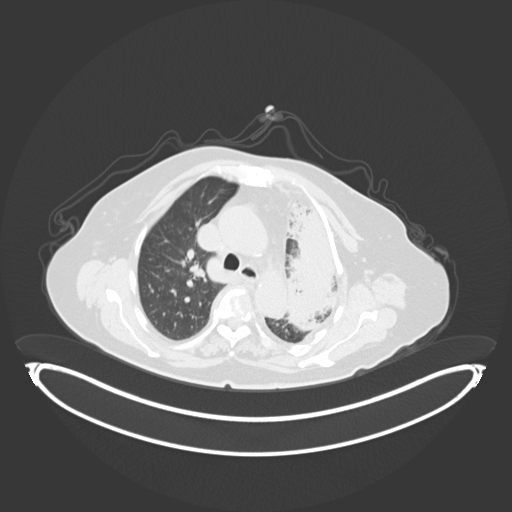
Chest CT, one axial slice. Slice 215 of 284 in the series (ordered by position). Reconstruction kernel B30f. Lung window (W 1500 / L -600 HU). 3 mm slice thickness. 512 × 512 image matrix, field of view 500 × 500 mm. Patient: female, 75 years. From the clinical record (not read from this slice): clinical TNM (as recorded): T3 N3 M1.
Annotated regions visible in this slice (bounding box drawn by a radiologist):
- lung tumour (recorded histology: adenocarcinoma): bounding box [x1, y1, x2, y2] px = [270, 189, 341, 337]